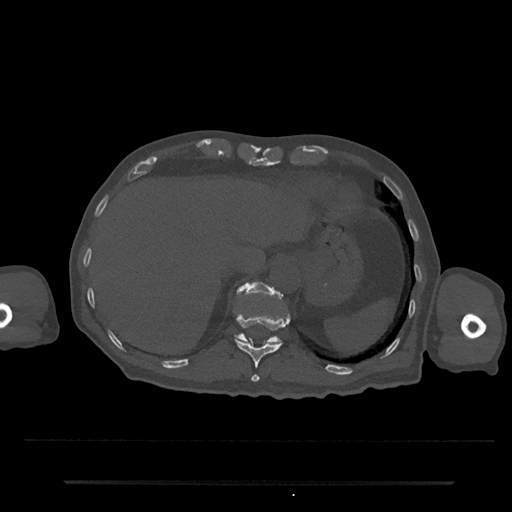
CT including the spine, one axial slice; slice 240 of 797 in the series (ordered by position); 120 kVp; bone window (W 1800 / L 400 HU); 0.5 mm slice thickness; 512 × 512 image matrix. Patient: male, 74 years. From the clinical record (not read from this slice): primary cancer: prostate.
Structures marked on this image (semi-automatic segmentation, software-assisted and operator-edited):
- T11 vertebra: bounding box (x1, y1, x2, y2) in pixels: (235, 314, 289, 382)
- T12 vertebra: (235, 282, 281, 344)